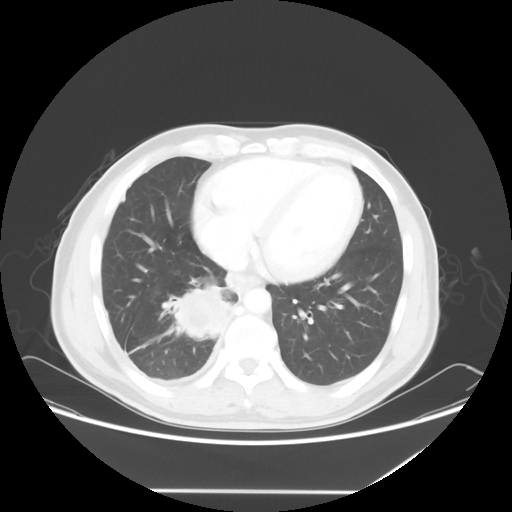
Chest CT, one axial slice. Position 21 of 60 along the scan axis. Reconstruction kernel STANDARD. Lung window (W 1500 / L -600 HU). 5 mm slice thickness. 512 × 512 image matrix, field of view 419 × 419 mm. Male patient, age 48 years. Case-level facts recorded for this patient, not image findings: clinical TNM (as recorded): T3 N3 M1a.
Structures marked on this image (rectangle marked by the reading radiologist):
- lung tumour (recorded histology: squamous cell carcinoma): bounding box [x1, y1, x2, y2] px = [164, 274, 234, 346]